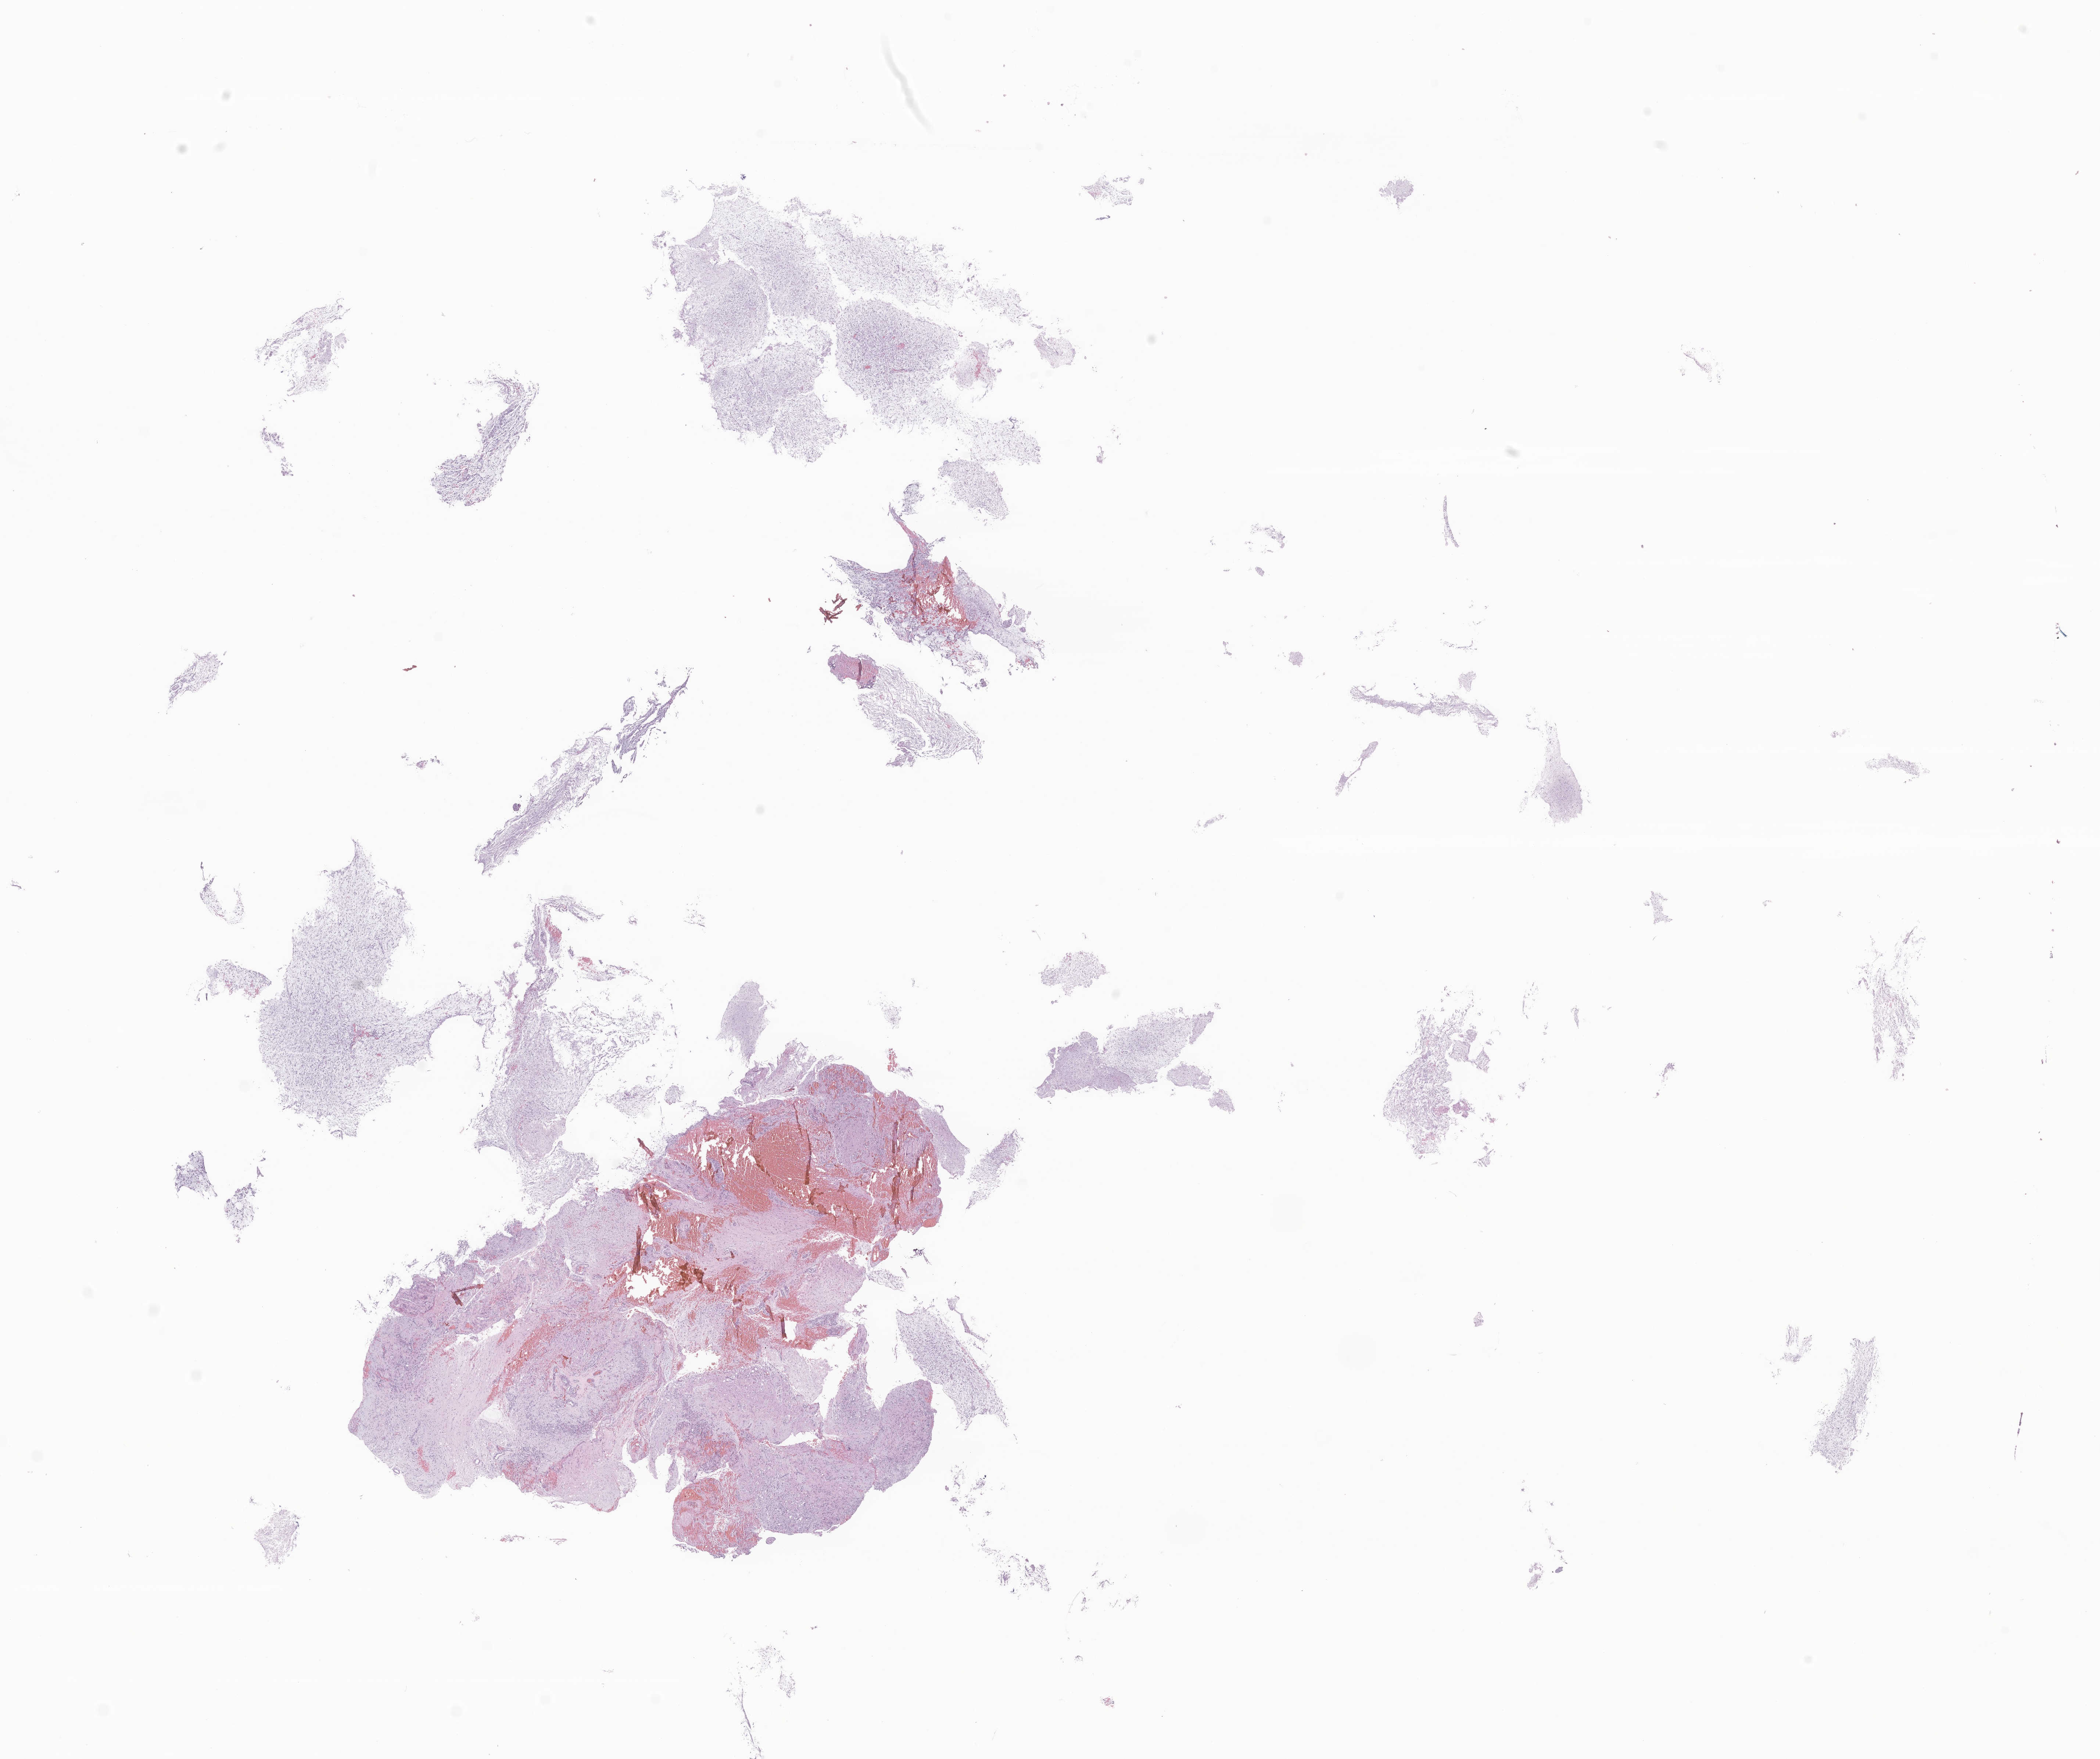
Hematoxylin and eosin (H&E) whole-slide image of tumor tissue from the spinal cord, whole scanned area (about 24.1 x 20.2 mm) shown as a low-resolution overview, formalin-fixed, paraffin-embedded (FFPE) tissue. Patient: male, age 113 months (9 years 5 months).
Diagnosis (ICD-O-3 morphology term): Pilocytic astrocytoma.